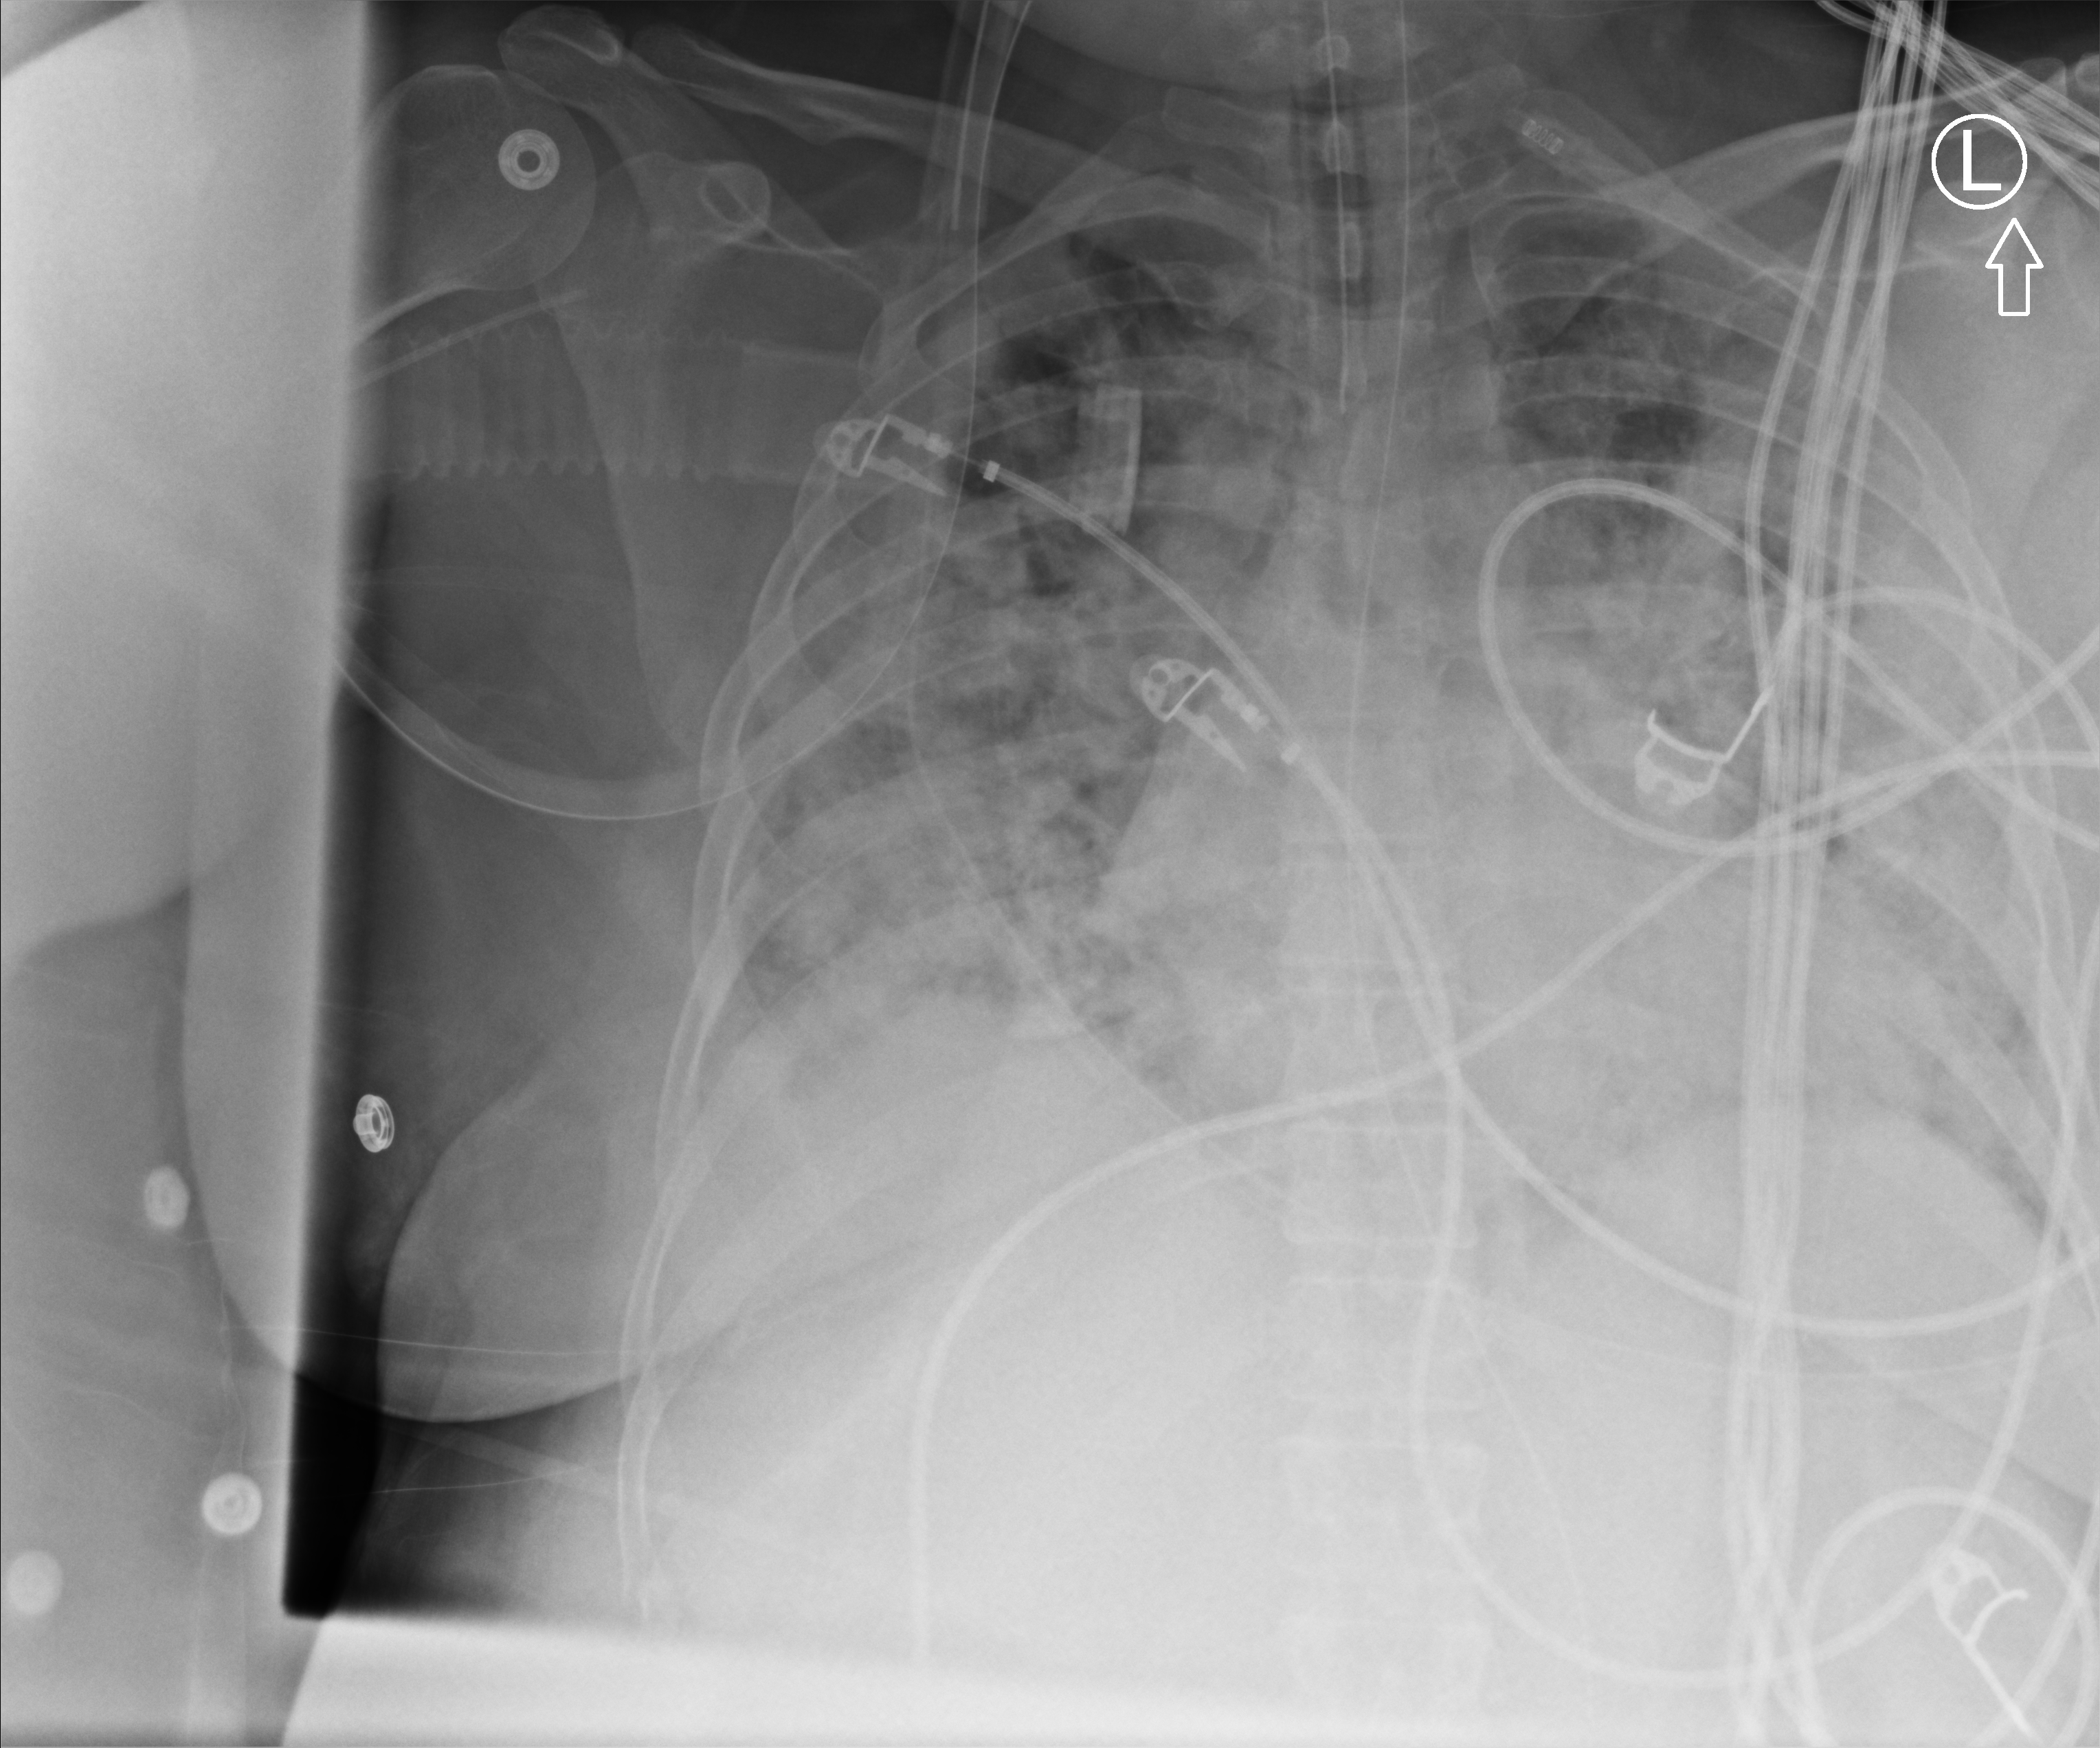
Bedside chest radiograph (computed radiography). Patient hospitalised with COVID-19; female, aged 18–59 years.
From the hospital-stay record, not from the radiograph (when in the stay this image was taken is not recorded): other chronic lung disease (admission record): no; length of hospital stay: 31 days; mechanically ventilated during this hospital stay: yes.